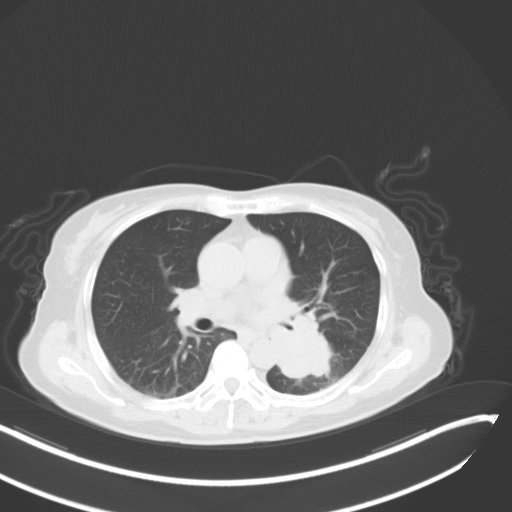
Chest CT, one axial slice; position 21 of 48 along the scan axis; reconstruction kernel B31f; 120 kVp; lung window (W 1500 / L -600 HU); 5 mm slice thickness; 512 × 512 image matrix. Female patient, age 64 years. From the clinical record (not read from this slice): clinical TNM (as recorded): T3 N1 M1; histopathological grade: G3.
Annotated regions visible in this slice (rectangle marked by the reading radiologist):
- lung tumour (recorded histology: small cell carcinoma): bounding box (x1, y1, x2, y2) in pixels: (262, 308, 337, 381)